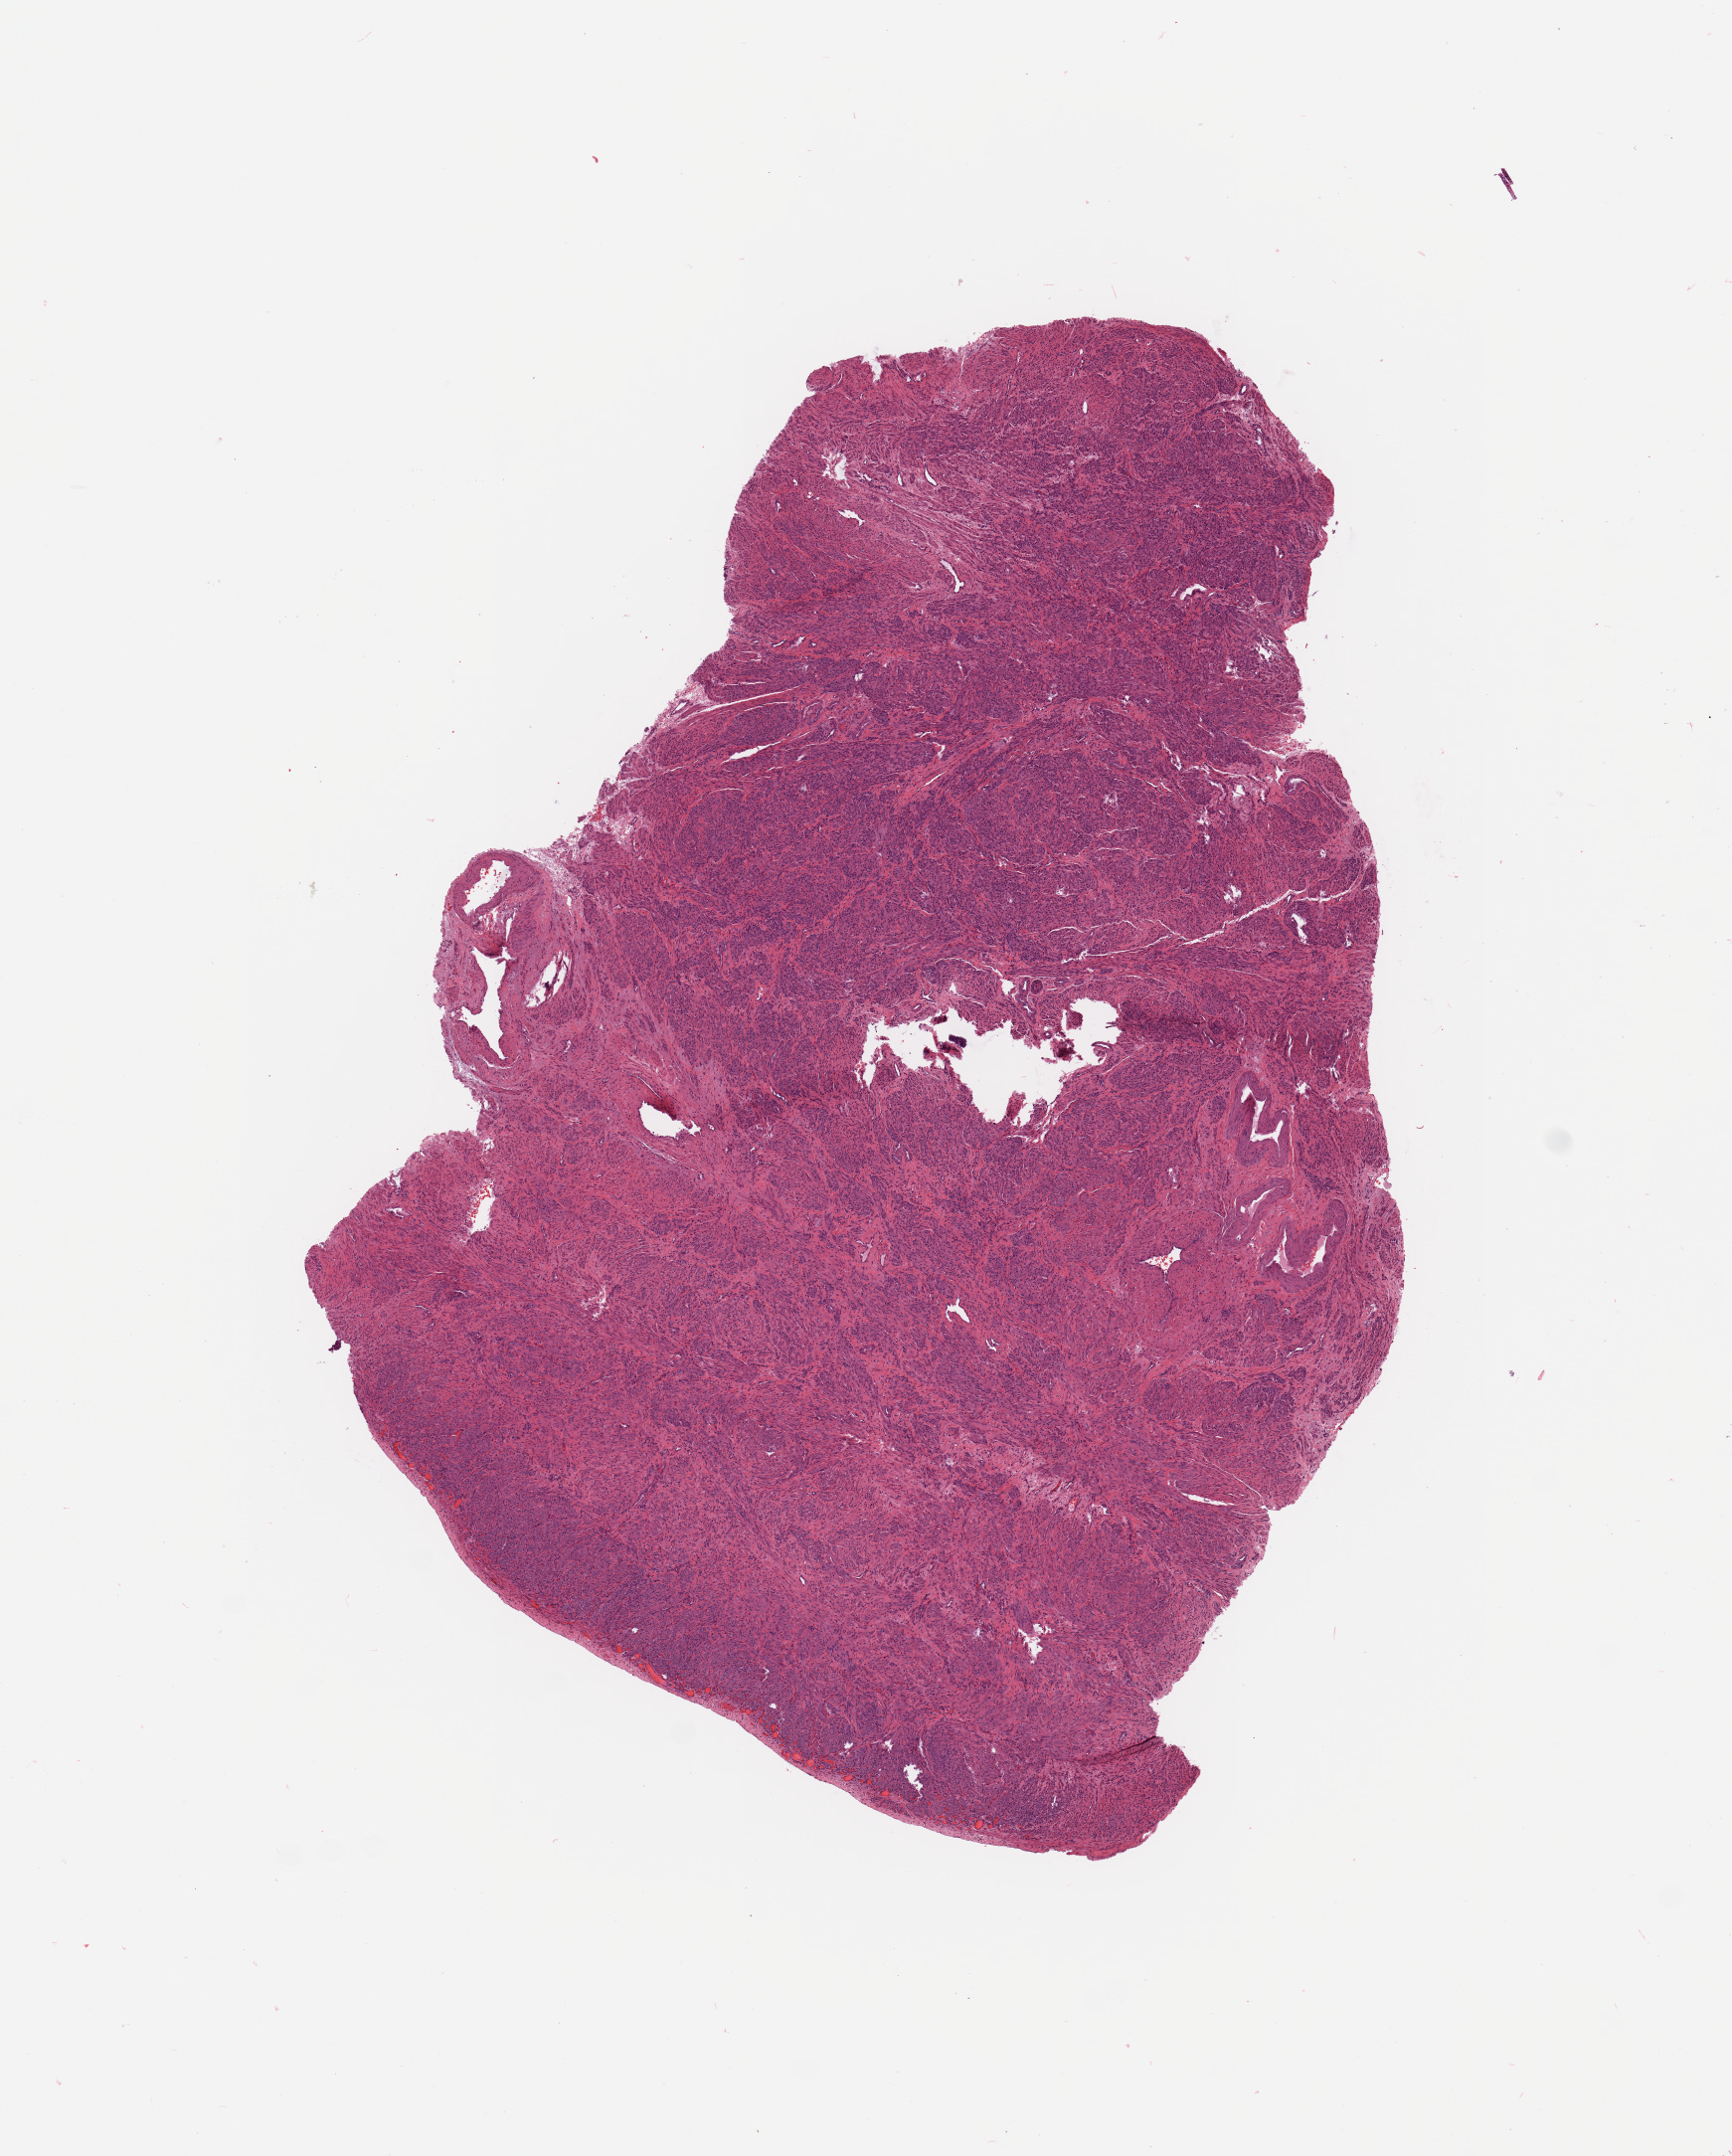
Digitized Hematoxylin and eosin (H&E) stained tissue section (whole slide), whole scanned area (about 6.9 x 8.6 mm) shown as a low-resolution overview, normal (non-tumour) tissue sample, uterus. 55-year-old female patient.
This section: normal (non-tumour) tissue from the same patient. Patient diagnosis: Endometrioid adenocarcinoma, NOS.